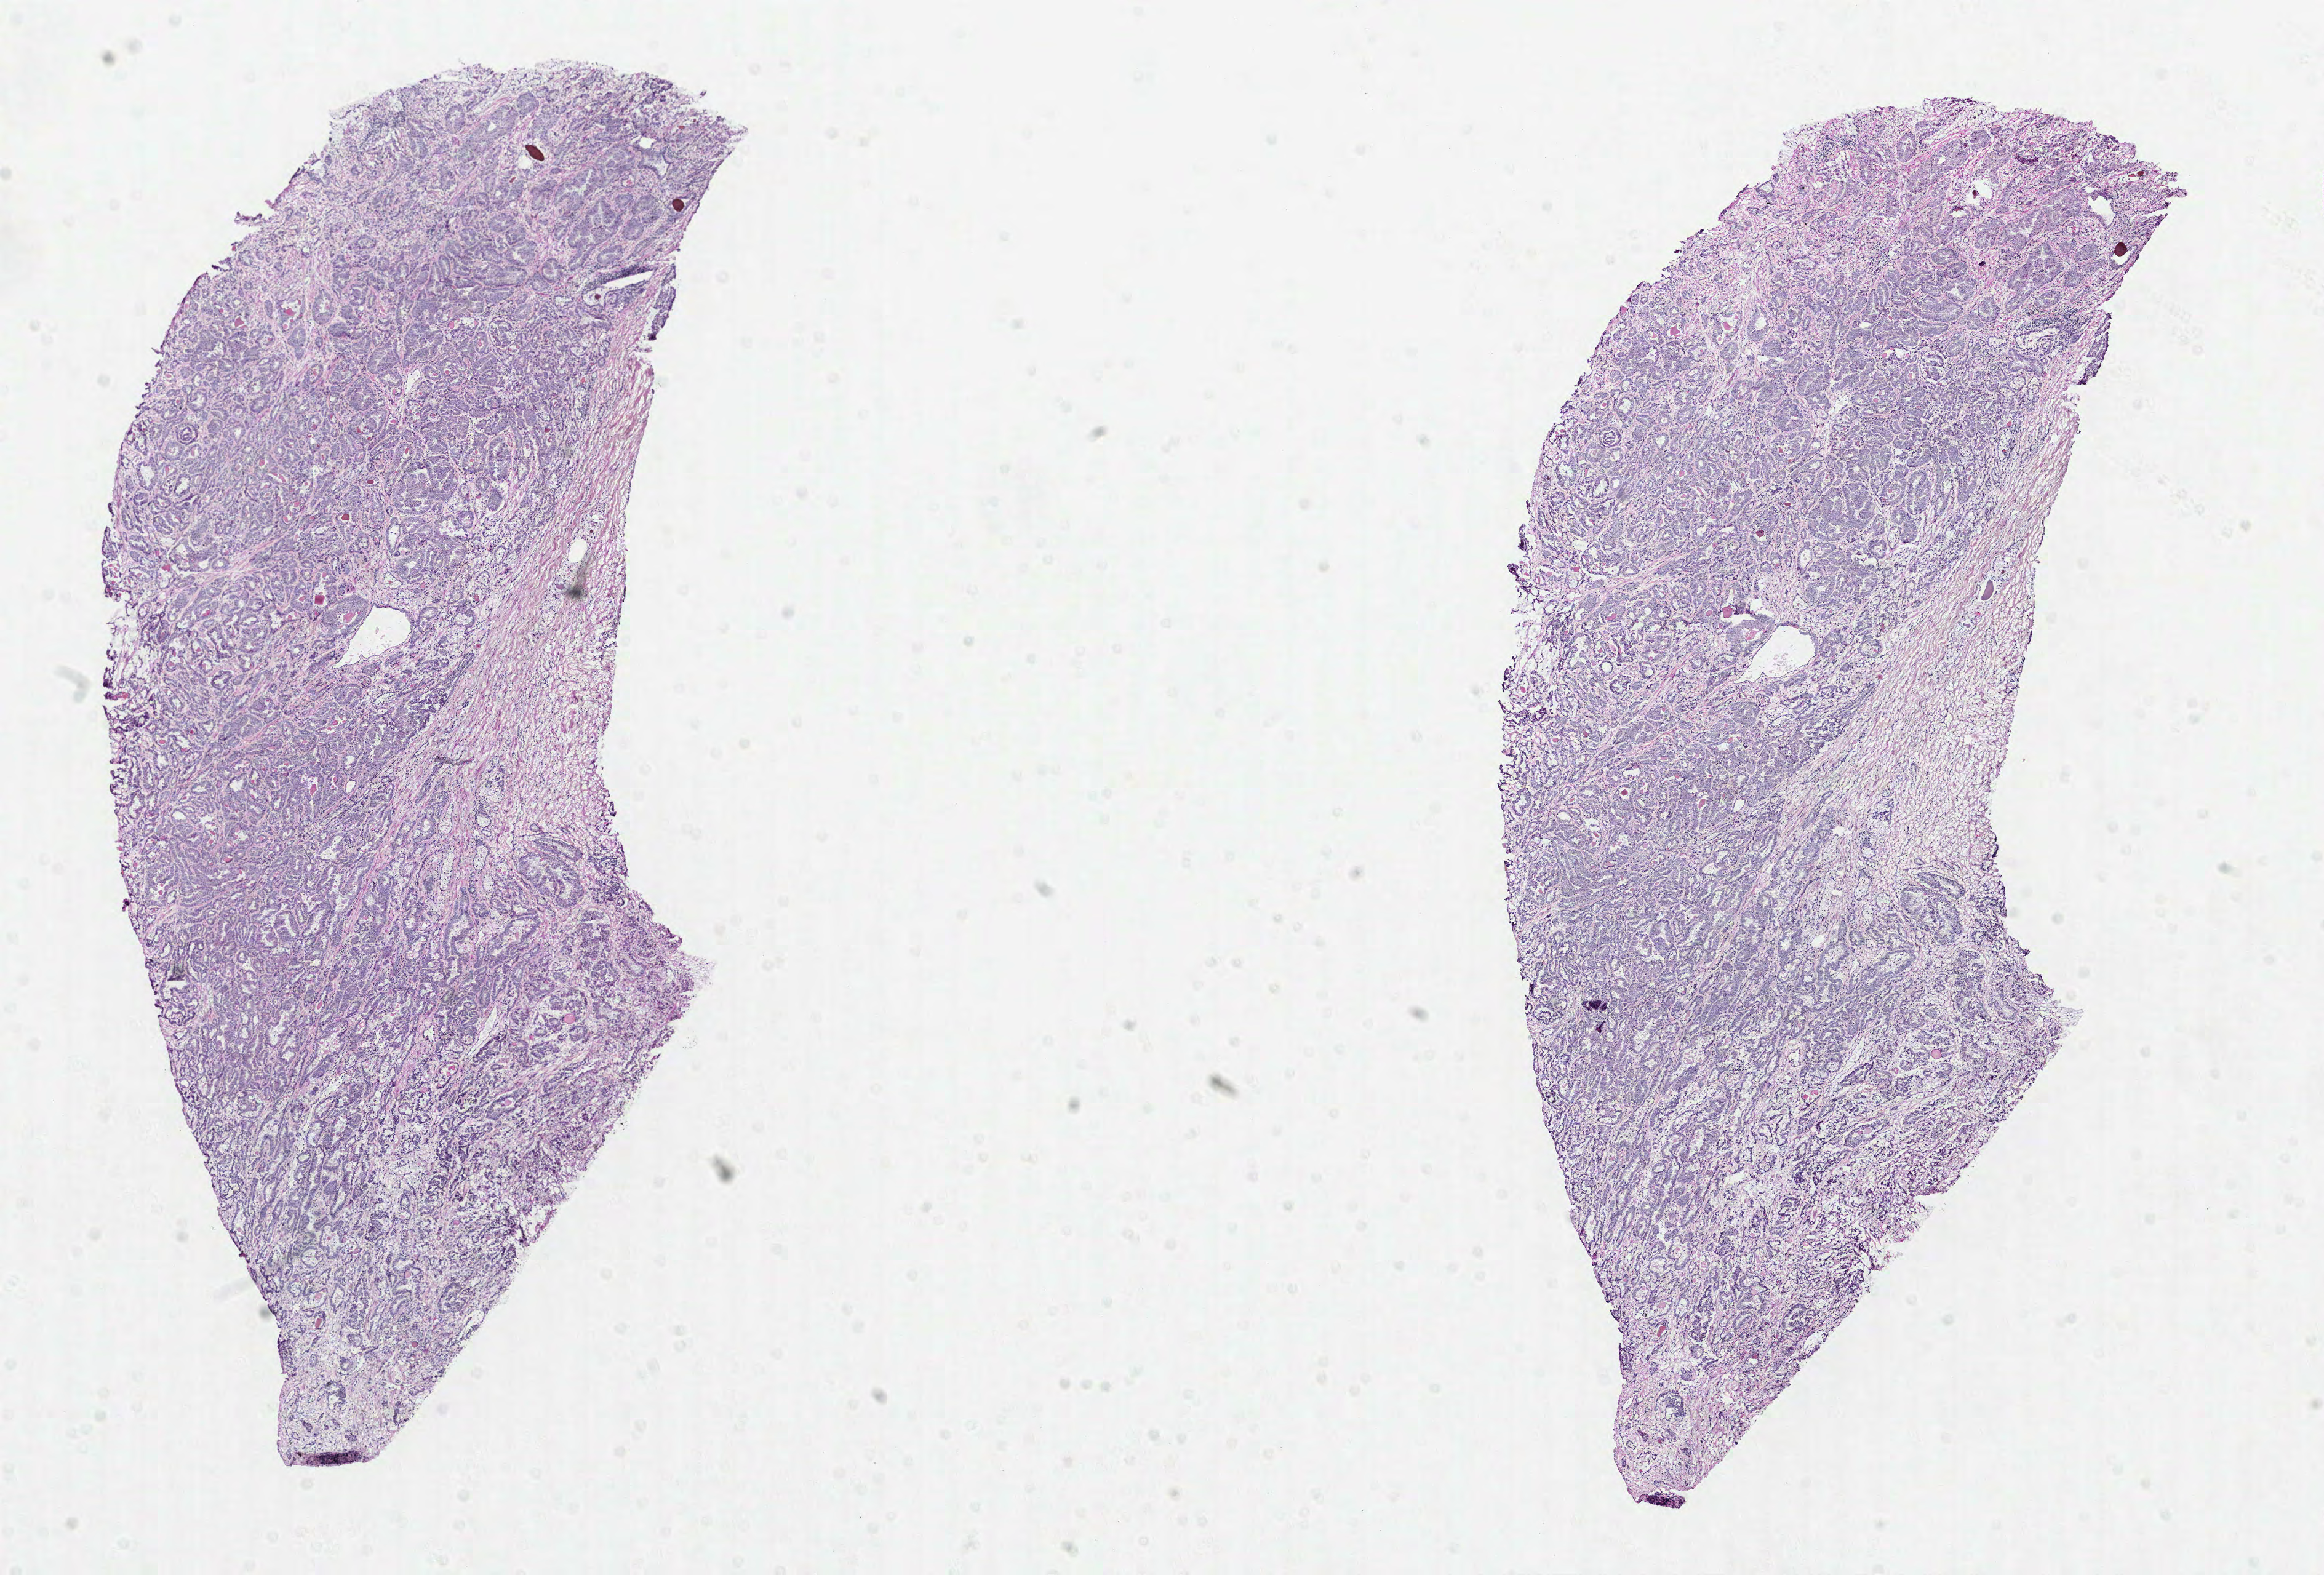
Whole-slide histology image, H&E-stained — whole scanned area (about 15.2 x 10.3 mm, acquisition: 40x scan) shown as a low-resolution overview; formalin-fixed paraffin-embedded (FFPE) diagnostic section; sample: primary tumour, prostate. Patient: male, age at initial diagnosis 73 years. Gleason score: 7 (4+3).
* lymph nodes positive (case pathology): 0 of 8 examined
* histologic diagnosis: Acinar cell carcinoma